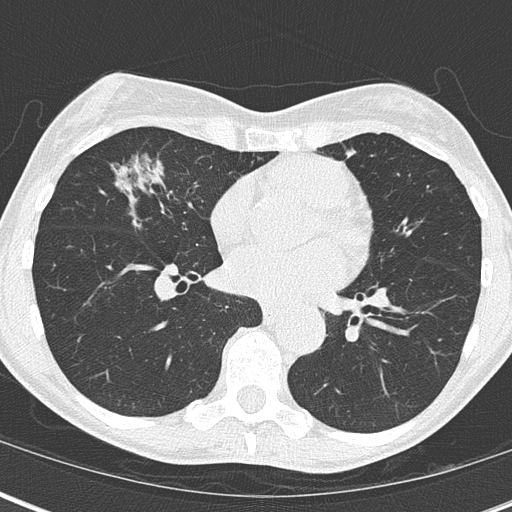
Chest CT (low-dose screening protocol), one axial image, third screening round (two years after baseline), lung window (W 1500 / L -600 HU), 2 mm slice thickness. Female participant, aged 67 years at enrolment. Current smoker at enrolment.
- Lesion marked by an expert reader, bounding box <96,148,198,247> (left, top, right, bottom; pixels).
- Screening reader's record for this exam (one nodule recorded; not confirmed to be the boxed lesion): non-calcified nodule or mass ≥4 mm, right middle lobe, 32 × 17 mm, mixed attenuation, pre-existing on the prior screen: yes; interval growth: yes.
- Official screen result: positive, other.
- Lung cancer was diagnosed 76 days after this screen: bronchiolo-alveolar adenocarcinoma, NOS, right middle lobe, well differentiated (G1), stage IA (AJCC 6th edition), 25 mm at pathology.